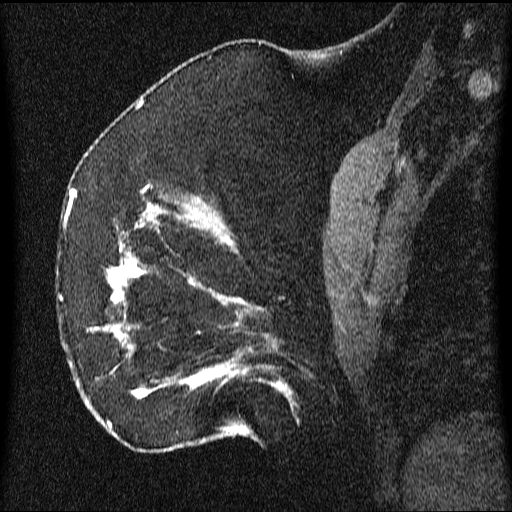
Breast MRI (dynamic contrast-enhanced), one sagittal slice. Slice 23 of 64 in the series (ordered by position). Dynamic contrast-enhanced series, image 2 of 3 at this slice position (ordered by acquisition). 1.5 T. TE 4.2 ms, TR 9.1 ms. 2.2 mm slice thickness. 512 × 512 image matrix. Female patient, age 52 years.
Structures marked on this image (semi-automatic segmentation, software-assisted and operator-edited):
- analysis volume of interest (the breast-tissue region the enhancement analysis was run in; not a lesion): bounding box (x1, y1, x2, y2) in pixels: (61, 203, 350, 438)
- tumour enhancement mask (voxels above the 70 % enhancement threshold inside the analysis volume of interest): (67, 203, 284, 438)